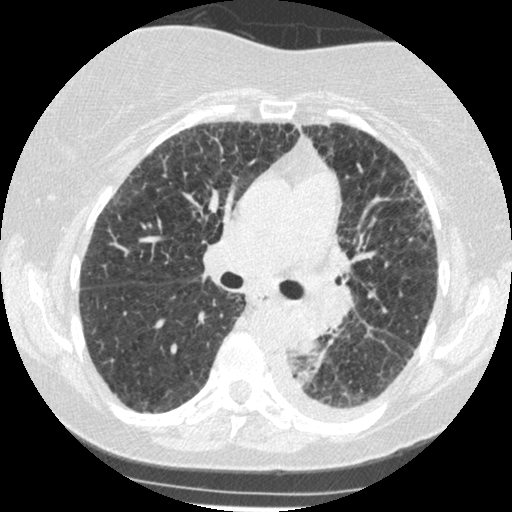
Low-dose screening chest CT, axial slice; third screening round (two years after baseline); lung window (W 1500 / L -600 HU); 1.25 mm slice thickness; standard (soft-tissue) reconstruction kernel (STANDARD); 512 × 512 image matrix. Female participant, aged 60 years at enrolment.
- Expert reader's lesion annotation, bounding box <269,308,342,373> (left, top, right, bottom; pixels).
- The exam's reader record, not a measurement of the box and not confirmed to be the same lesion: non-calcified nodule or mass ≥4 mm, left lower lobe, 54 × 38 mm, smooth margins, soft tissue attenuation, pre-existing on the prior screen: yes; interval growth: yes.
- Official screen result: positive, other.
- Later outcome: lung cancer diagnosed 15 days after this screen — small cell carcinoma, NOS, left lower lobe, undifferentiated (G4), stage IV (AJCC 6th edition), 69 mm at pathology.